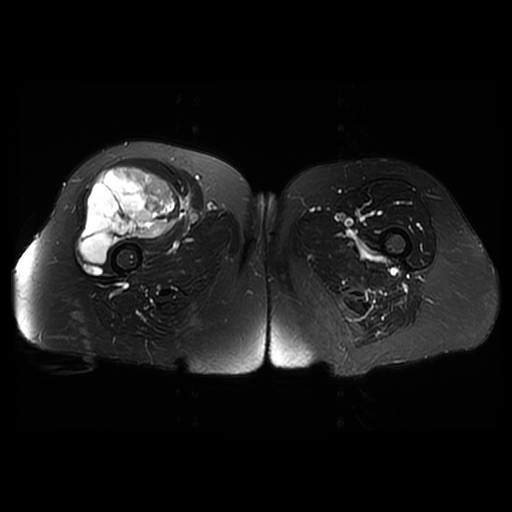
MRI of an extremity soft-tissue mass, one axial slice; slice 27 of 42 in the series (ordered by position); T2-weighted fat-saturated; 512 × 512 image matrix, field of view 440 × 440 mm. Female patient. From the clinical record (not read from this slice): histological type: pleiomorphic undifferentiated sarcoma; grade: high; site of the primary tumour: right quadricep.
Annotated regions visible in this slice (outlined manually by an expert reader):
- gross tumour volume including surrounding oedema: bounding box [x1, y1, x2, y2] px = [79, 167, 179, 264]
- gross tumour volume (mass): [79, 167, 179, 264]